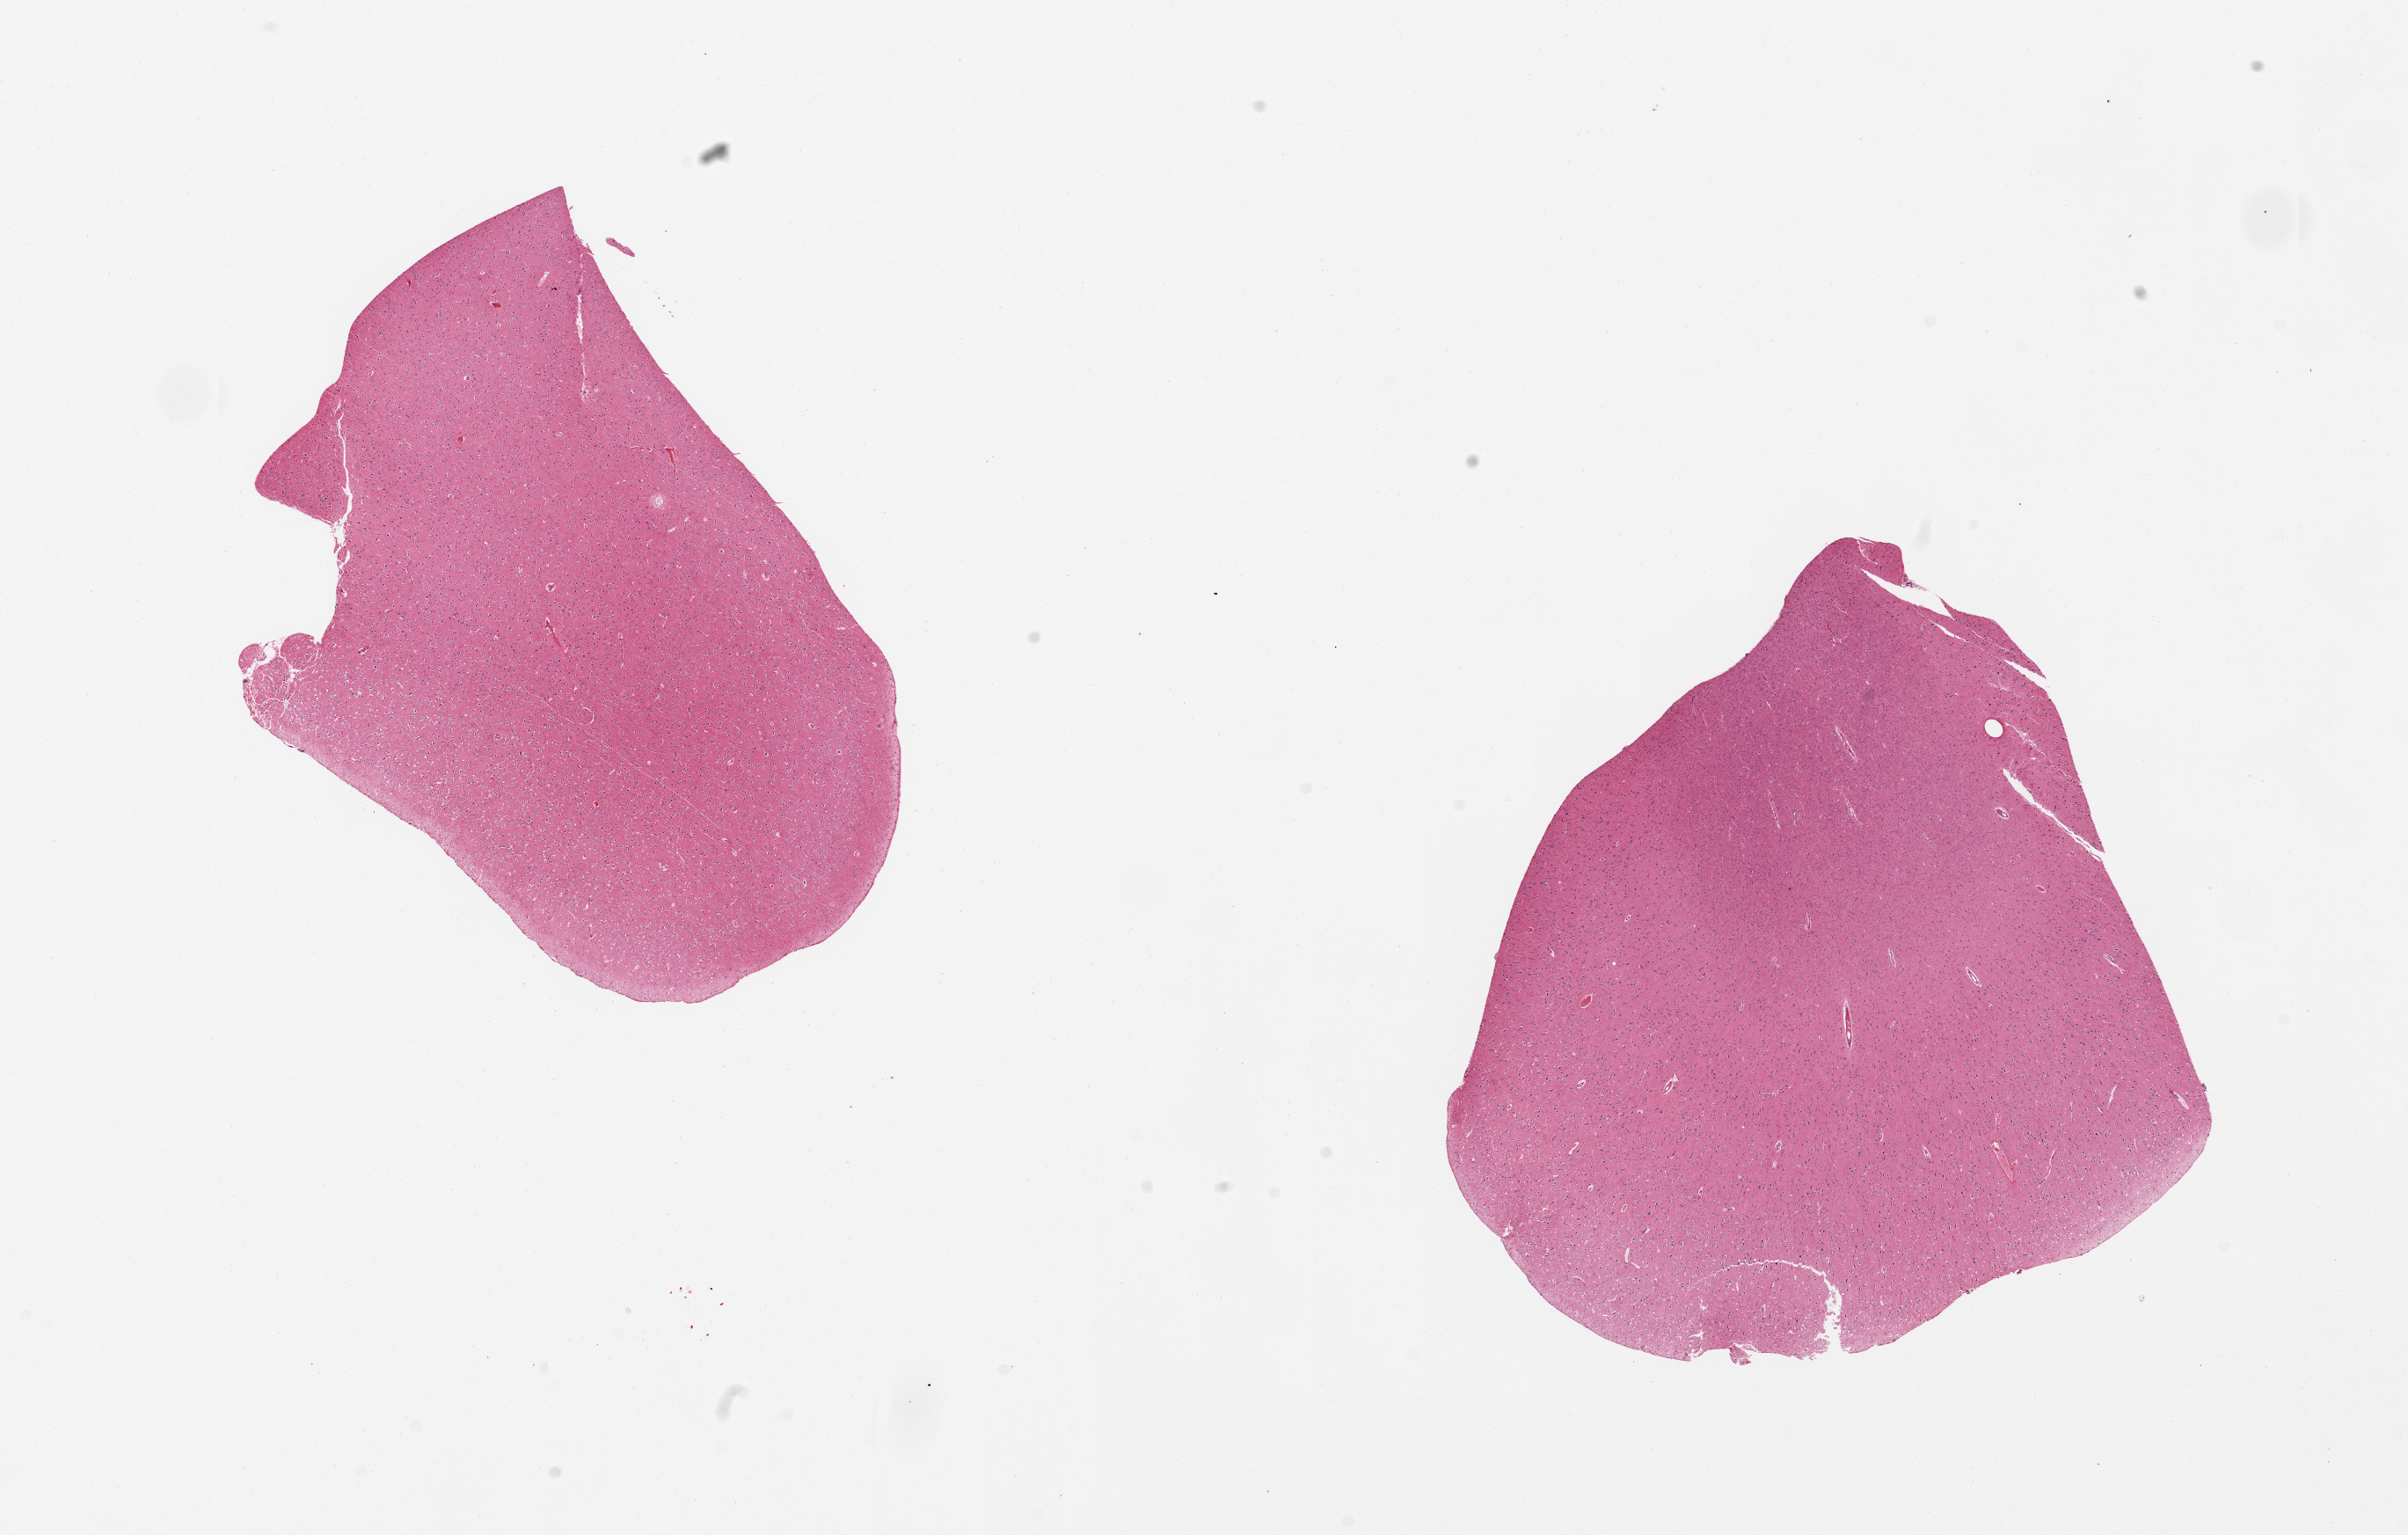
Whole-slide image, haematoxylin and eosin stain — whole scanned area (about 21.7 x 13.8 mm, from a 20x scan) shown as a low-resolution overview. PAXgene-fixed paraffin-embedded (PFPE) section. Sampled site (target tissue): cerebral cortex. Tissue donor sample. Donor: male.
Reviewer comment on this tissue sample: 2 pieces.